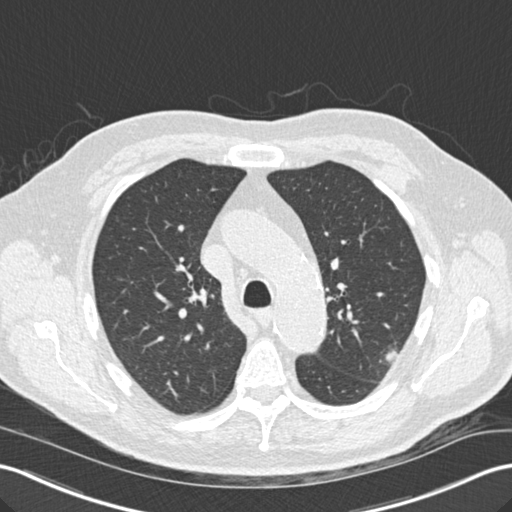
Chest CT (low-dose screening protocol), one axial image; third annual screen; lung window (W 1500 / L -600 HU); 2 mm slice thickness; standard (soft-tissue) reconstruction kernel (B30f). Male participant, aged 67 years at enrolment. Former smoker at enrolment.
Expert reader's lesion annotation, box from (x=365, y=335) to (x=408, y=372) px. The screening reader recorded 2 non-calcified nodules or masses ≥4 mm on this exam; which of them this box marks is not recorded. Lung cancer was diagnosed 55 days after this screen: squamous cell carcinoma, large cell, nonkeratinizing, NOS, left upper lobe, moderately differentiated (G2), stage IA (AJCC 6th edition), 15 mm at pathology.